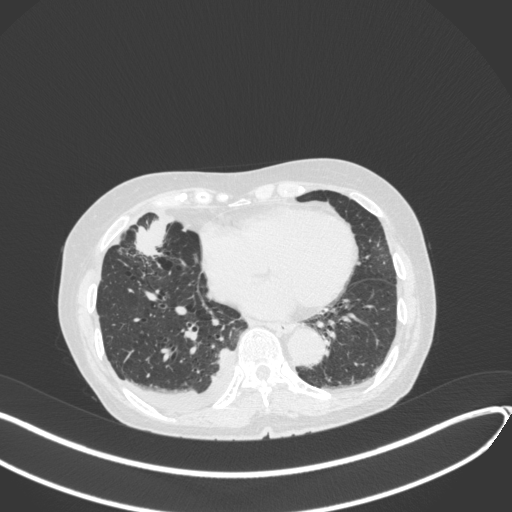
Chest CT, one axial slice; slice 134 of 418 in the series (ordered by position); reconstruction kernel B31f; lung window (W 1500 / L -600 HU); 1 mm slice thickness; 512 × 512 image matrix. Patient: female, 75 years. Case-level facts recorded for this patient, not image findings: clinical TNM (as recorded): T2a N3 M0.
Outlined on this slice (bounding box drawn by a radiologist):
- lung tumour (recorded histology: adenocarcinoma): bounding box <130,216,178,261> (left, top, right, bottom; pixels)